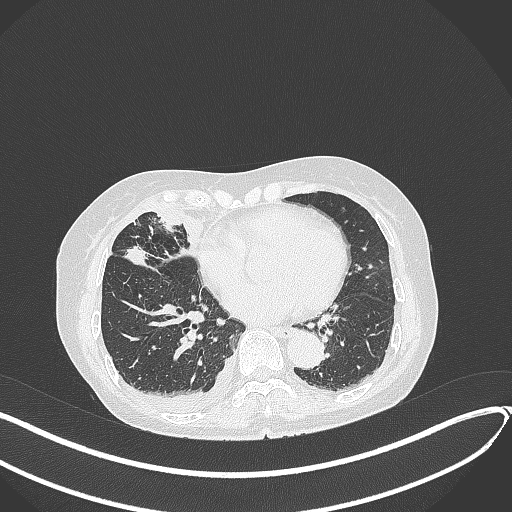
Chest CT, one axial slice. Slice 154 of 418 in the series (ordered by position). Lung window (W 1500 / L -600 HU). 1 mm slice thickness. 512 × 512 image matrix, field of view 400 × 400 mm. Female patient, age 75 years. From the clinical record (not read from this slice): clinical TNM (as recorded): T2a N3 M0.
Outlined on this slice (rectangle marked by the reading radiologist):
- lung tumour (recorded histology: adenocarcinoma): bounding box (x1, y1, x2, y2) in pixels: (120, 243, 148, 267)